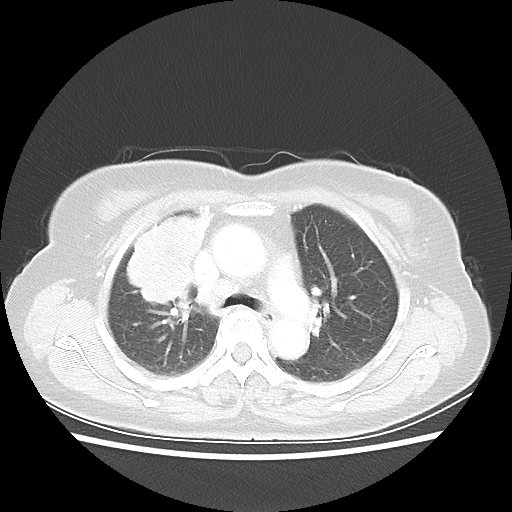
Chest CT, one axial slice; slice 36 of 55 in the series (ordered by position); reconstruction kernel LUNG; lung window (W 1500 / L -600 HU); 512 × 512 image matrix, field of view 337 × 337 mm. Patient: female, 62 years. Case-level facts recorded for this patient, not image findings: clinical TNM (as recorded): T4 N3 M0.
Outlined on this slice (bounding box drawn by a radiologist):
- lung tumour (recorded histology: squamous cell carcinoma): bounding box (x1, y1, x2, y2) in pixels: (115, 200, 214, 307)